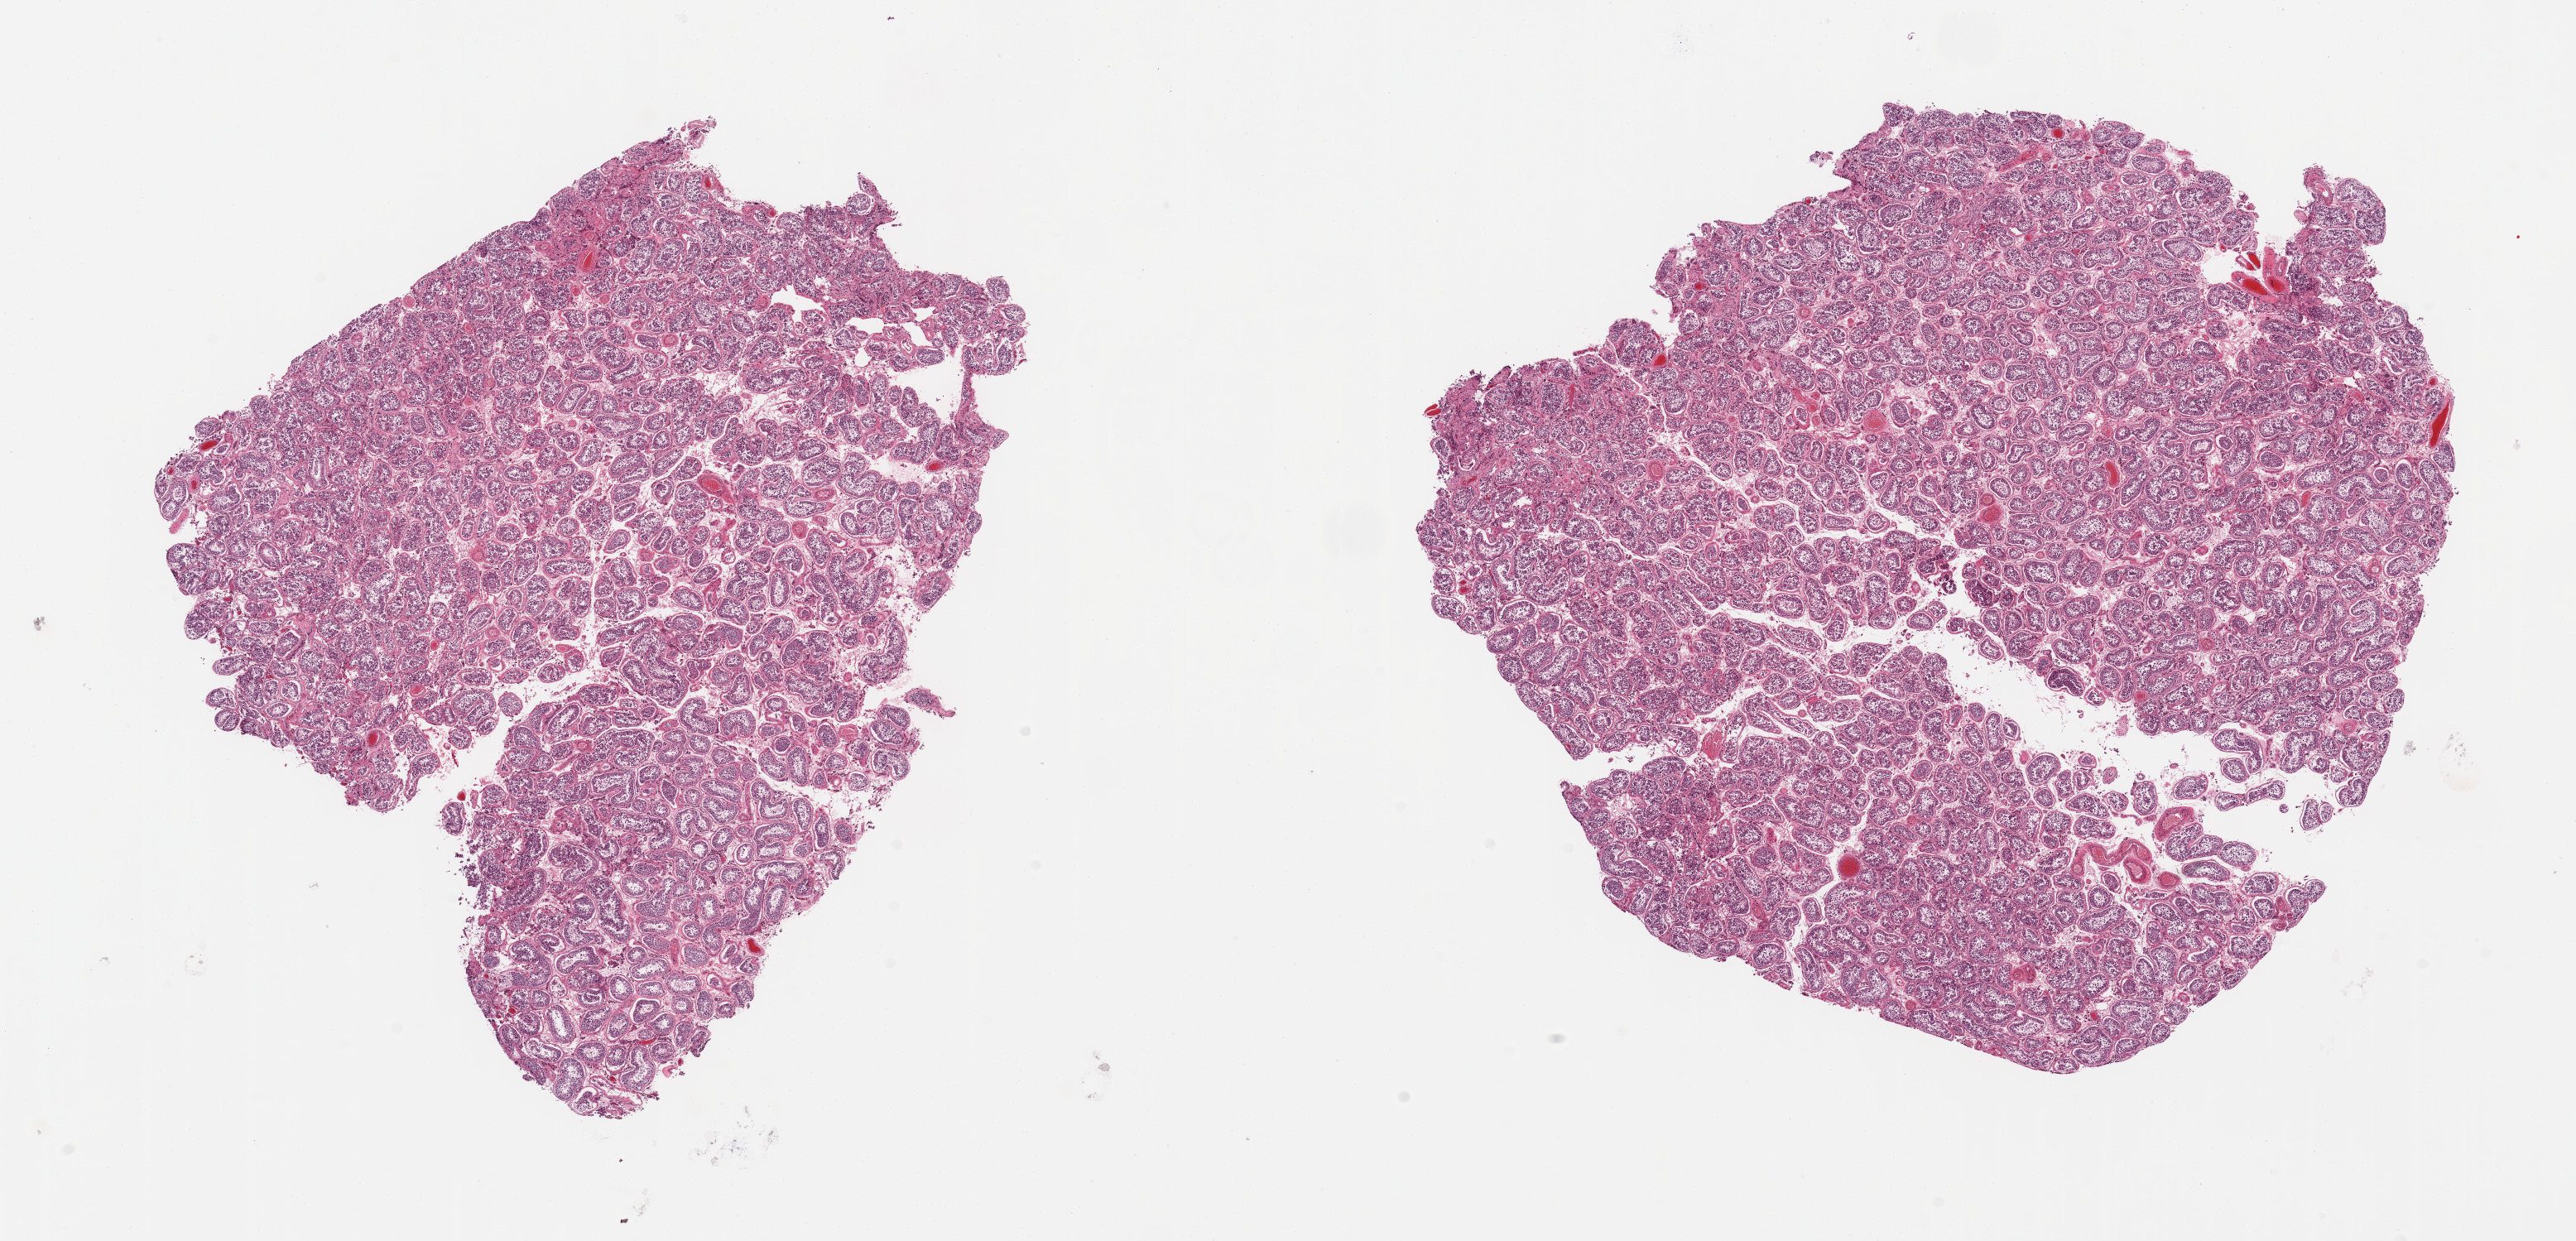
Whole-slide image, H&E stain, shown as a low-resolution overview of the whole scanned area (about 24.6 x 11.9 mm), PAXgene-fixed paraffin-embedded (PFPE) section, section of testis (target tissue), tissue donor sample.
Reviewer comment on this tissue sample: 2 pieces, approaching score '2'. Spermatogenesis is present but appears reduced.